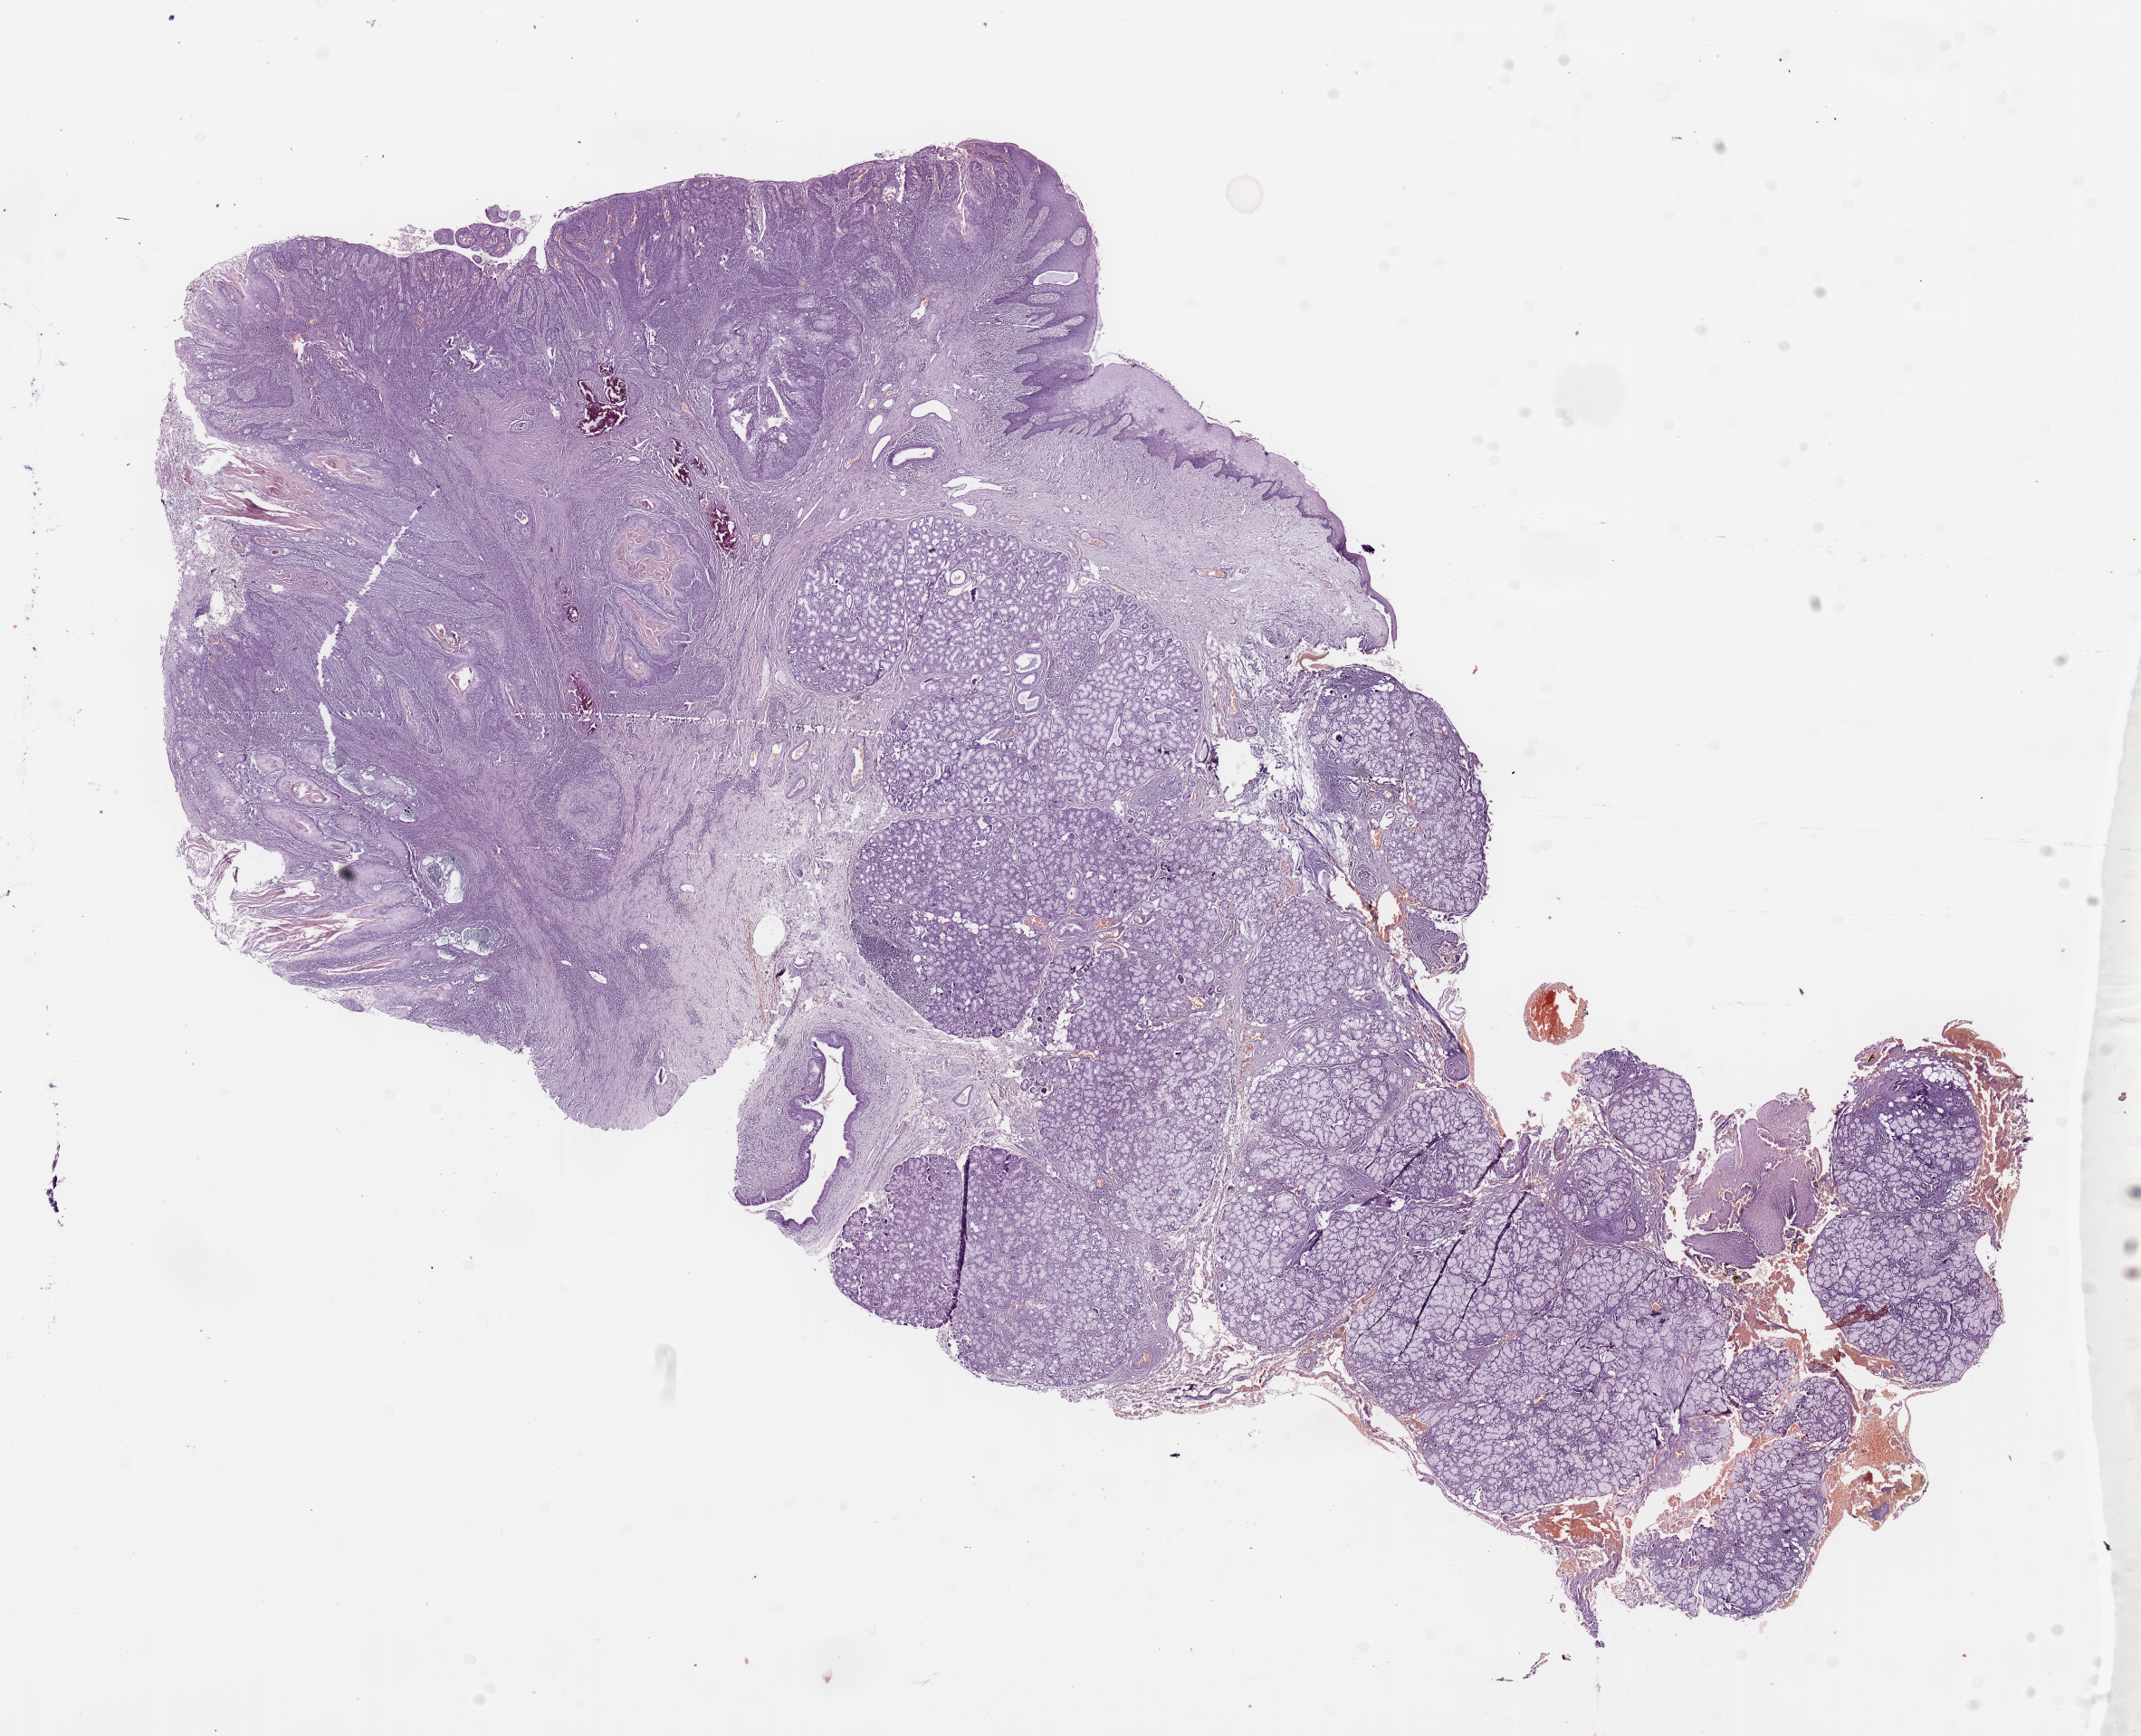
Digitized H&E tissue section (whole slide) — a low-resolution overview of the entire scanned area, about 18.7 x 15.2 mm (slide scanned at 20x); head and neck, tissue type not recorded. Male, 59 y/o.
Patient diagnosis: Squamous cell carcinoma, NOS.